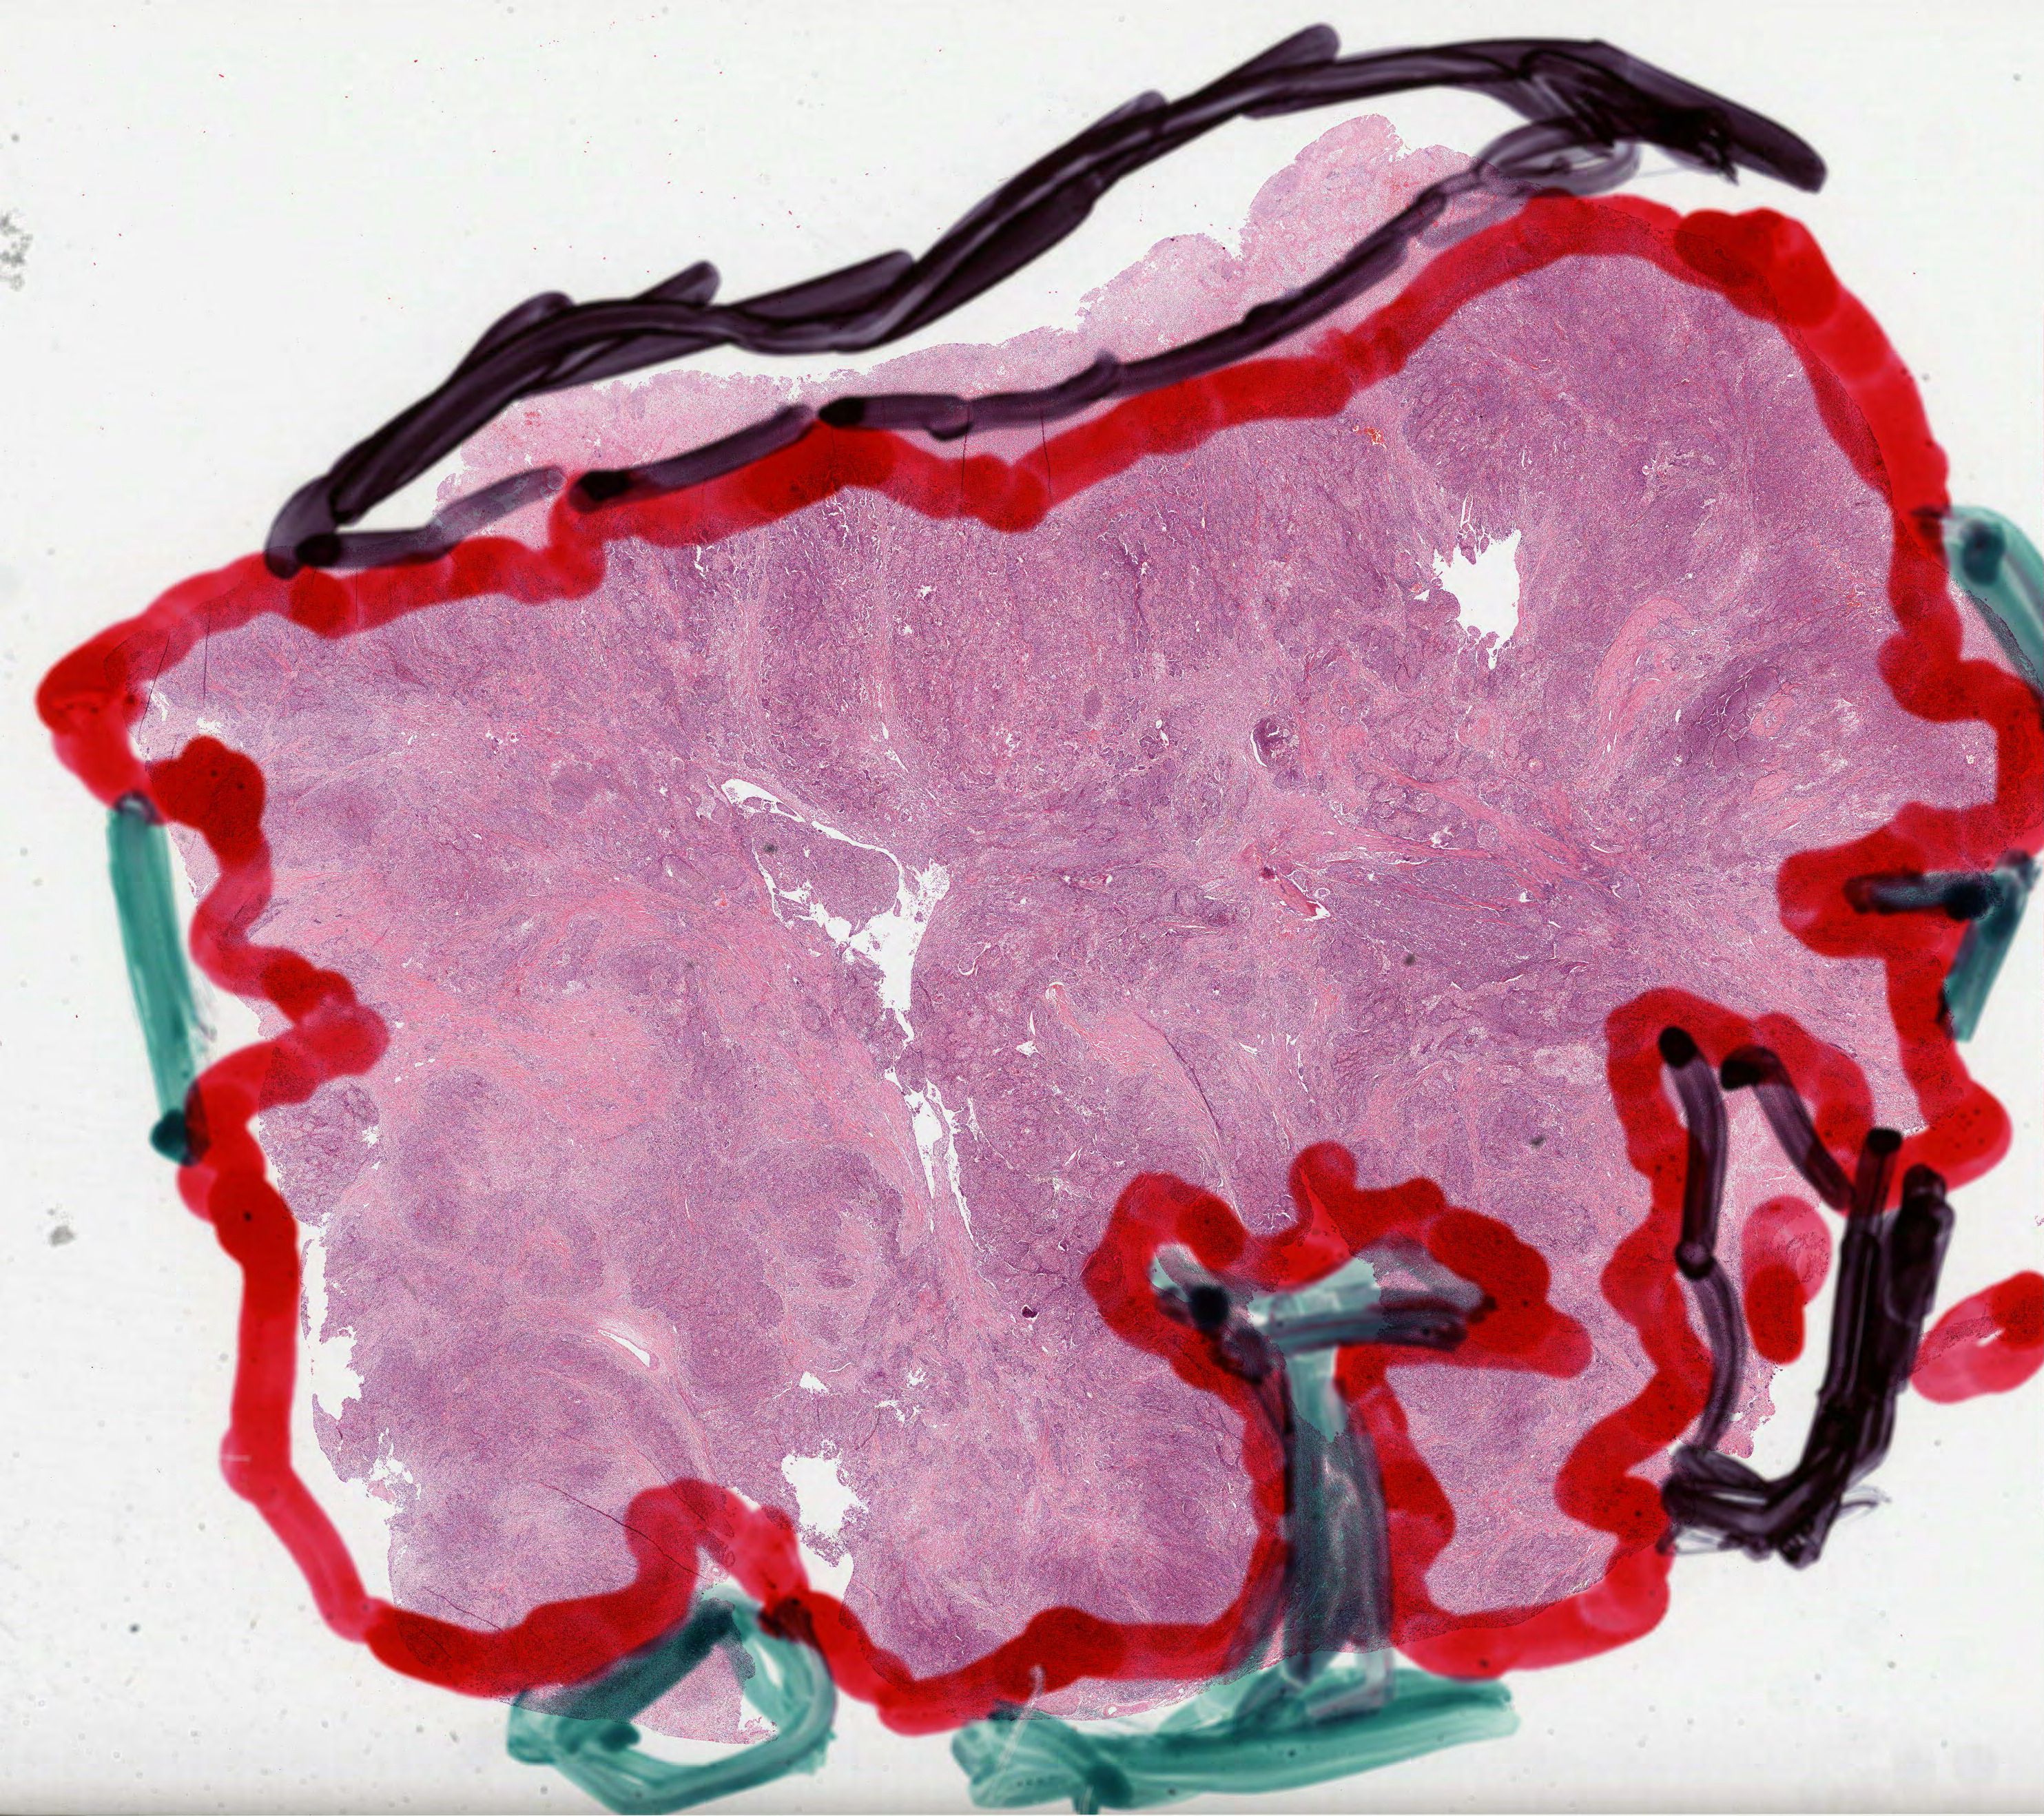
Digitized H&E tissue section (whole slide) — whole scanned area (about 23.9 x 21.3 mm, from a 40x scan) shown as a low-resolution overview, FFPE section, sample: primary tumour, stomach. Patient: female, age at initial diagnosis 64 years.
Diagnosis: Adenocarcinoma, NOS (cardia, NOS).